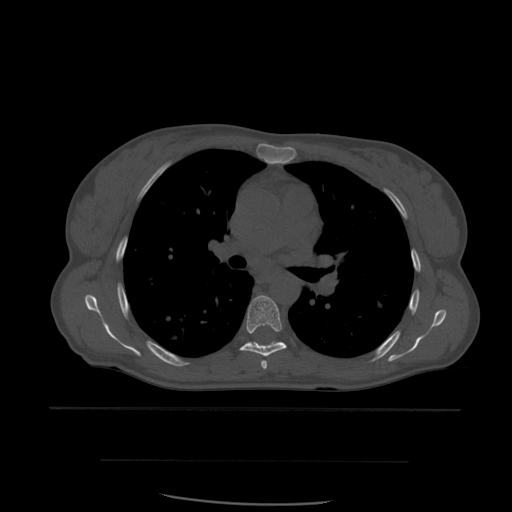
CT including the spine, one axial slice; position 393 of 574 along the scan axis; bone window (W 1800 / L 400 HU); 512 × 512 image matrix. Patient age 48 years. Case-level facts recorded for this patient, not image findings: primary cancer: lung.
Structures marked on this image (semi-automatic segmentation, software-assisted and operator-edited):
- T5 vertebra: box from (x=261, y=360) to (x=268, y=370) px
- T6 vertebra: (x=240, y=295)–(x=287, y=357)
- T7 vertebra: (x=255, y=342)–(x=279, y=343)